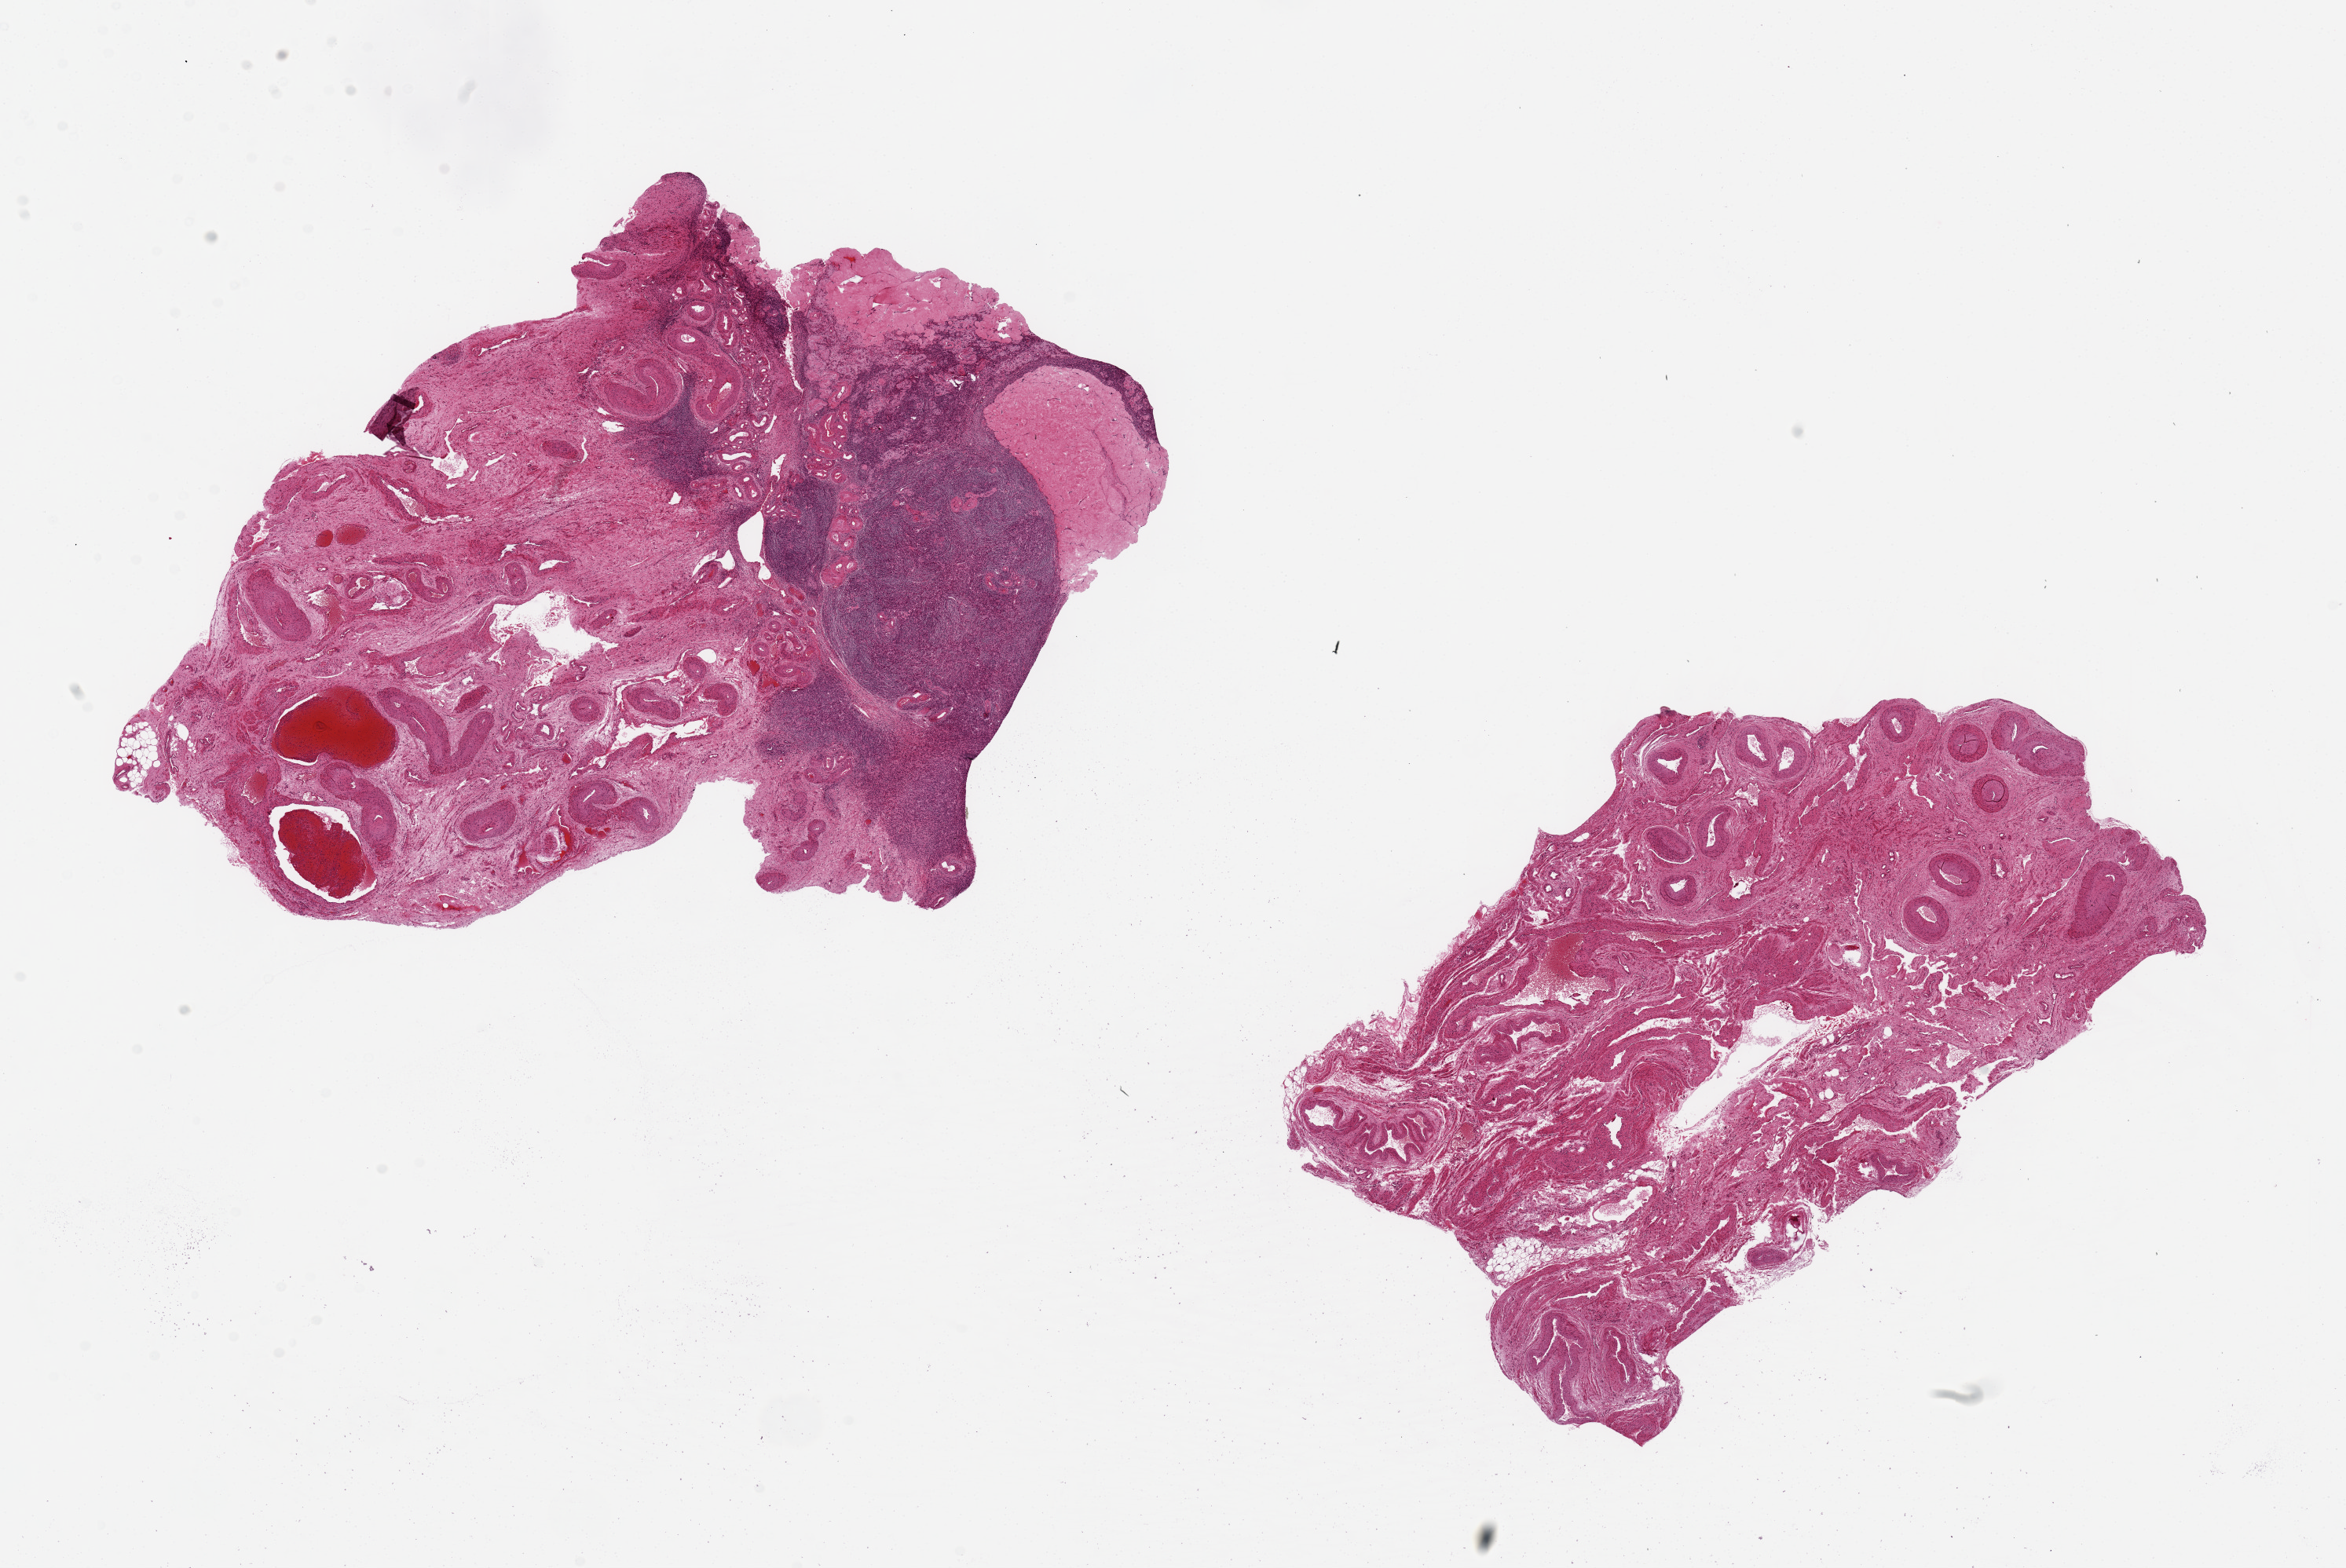
Digitized haematoxylin and eosin-stained section, a low-resolution overview of the entire scanned area, about 23.6 x 15.8 mm, PAXgene-fixed paraffin-embedded (PFPE) section, target tissue: ovary, tissue donor sample.
Review note (as recorded): 2 pieces ~9x6mm; One is post menopausal cortex and medulla, the other is all medullary elements (supporting vessels/stroma).